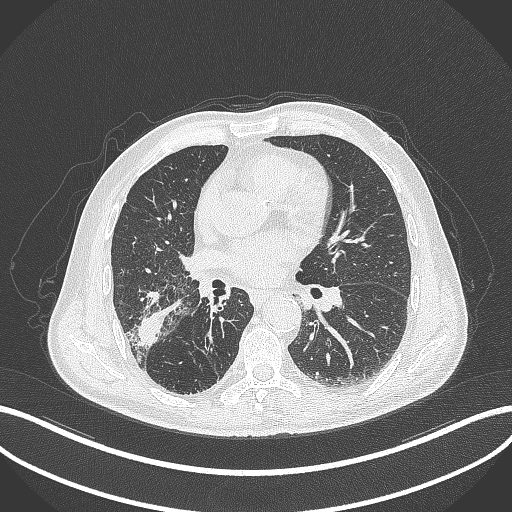
Chest CT, one axial slice. Position 209 of 429 along the scan axis. Lung window (W 1500 / L -600 HU). 1 mm slice thickness. 512 × 512 image matrix, field of view 400 × 400 mm. Patient: male, 72 years. Case-level facts recorded for this patient, not image findings: clinical TNM (as recorded): T3 N2 M0.
Annotated regions visible in this slice (bounding box drawn by a radiologist):
- lung tumour (recorded histology: adenocarcinoma): bounding box [x1, y1, x2, y2] px = [131, 310, 165, 349]